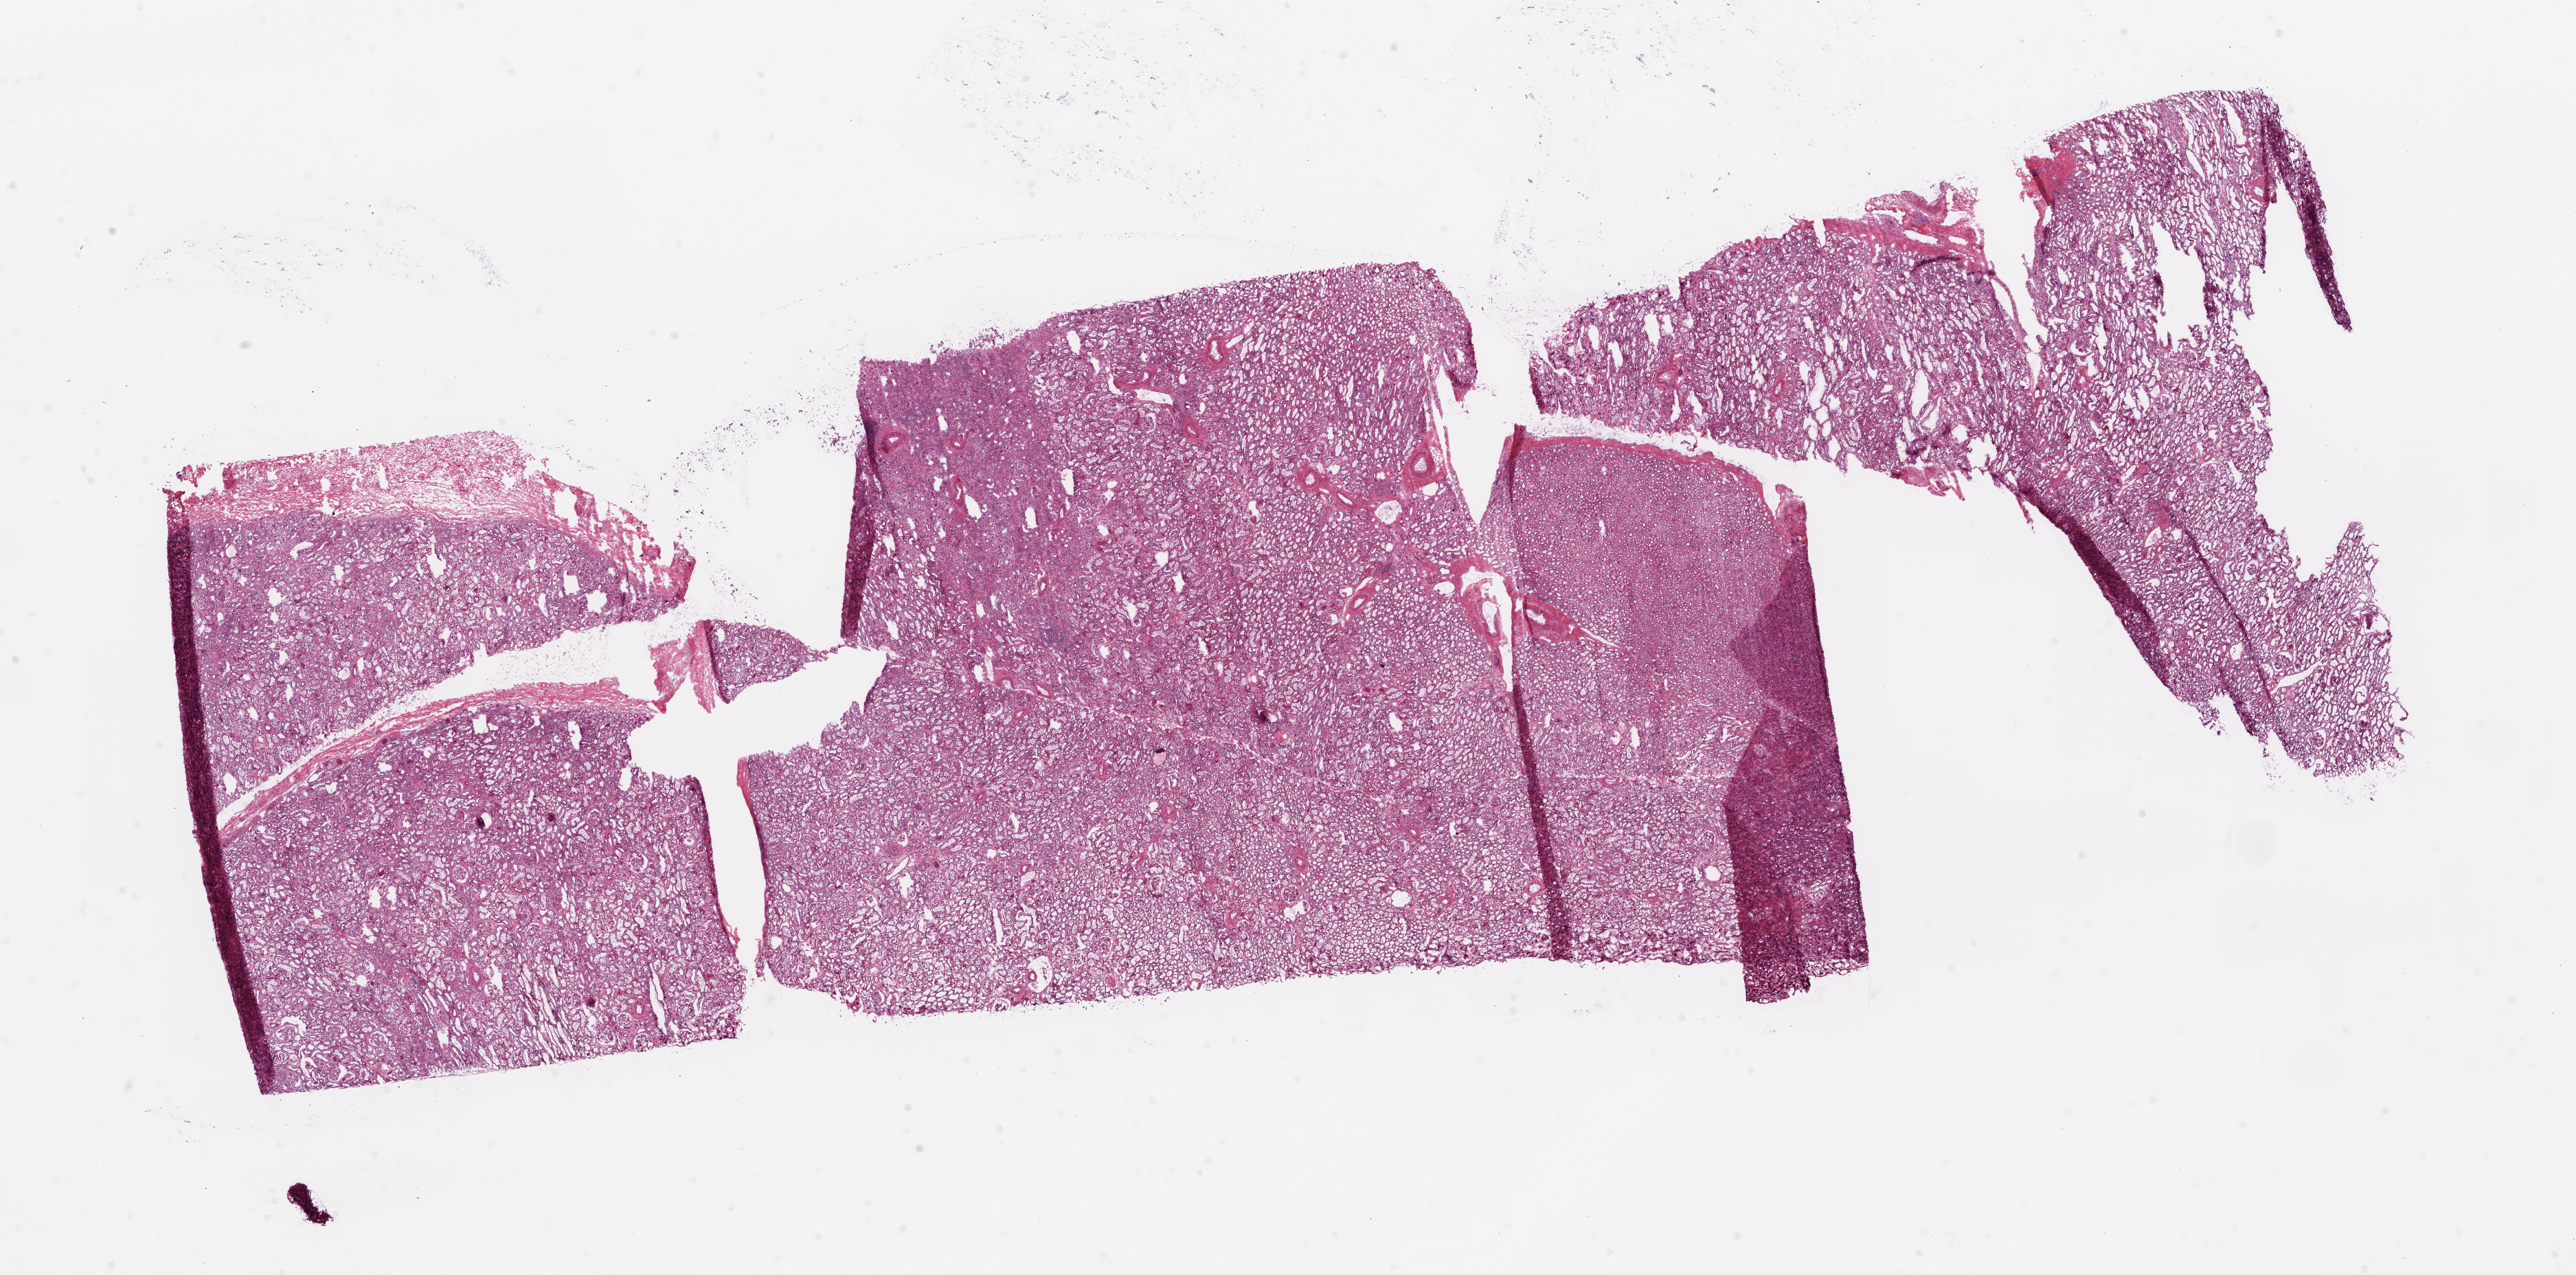
Hematoxylin and eosin (H&E) stained whole-slide image, whole scanned area (about 30.1 x 14.9 mm) shown as a low-resolution overview, frozen section from the bottom of the tissue portion, solid tissue normal (non-tumour tissue) sample from the kidney. Male patient; age at initial diagnosis 47 years.
This section: solid tissue normal (non-tumour) sample from the same patient. Patient diagnosis: Clear cell adenocarcinoma, NOS.